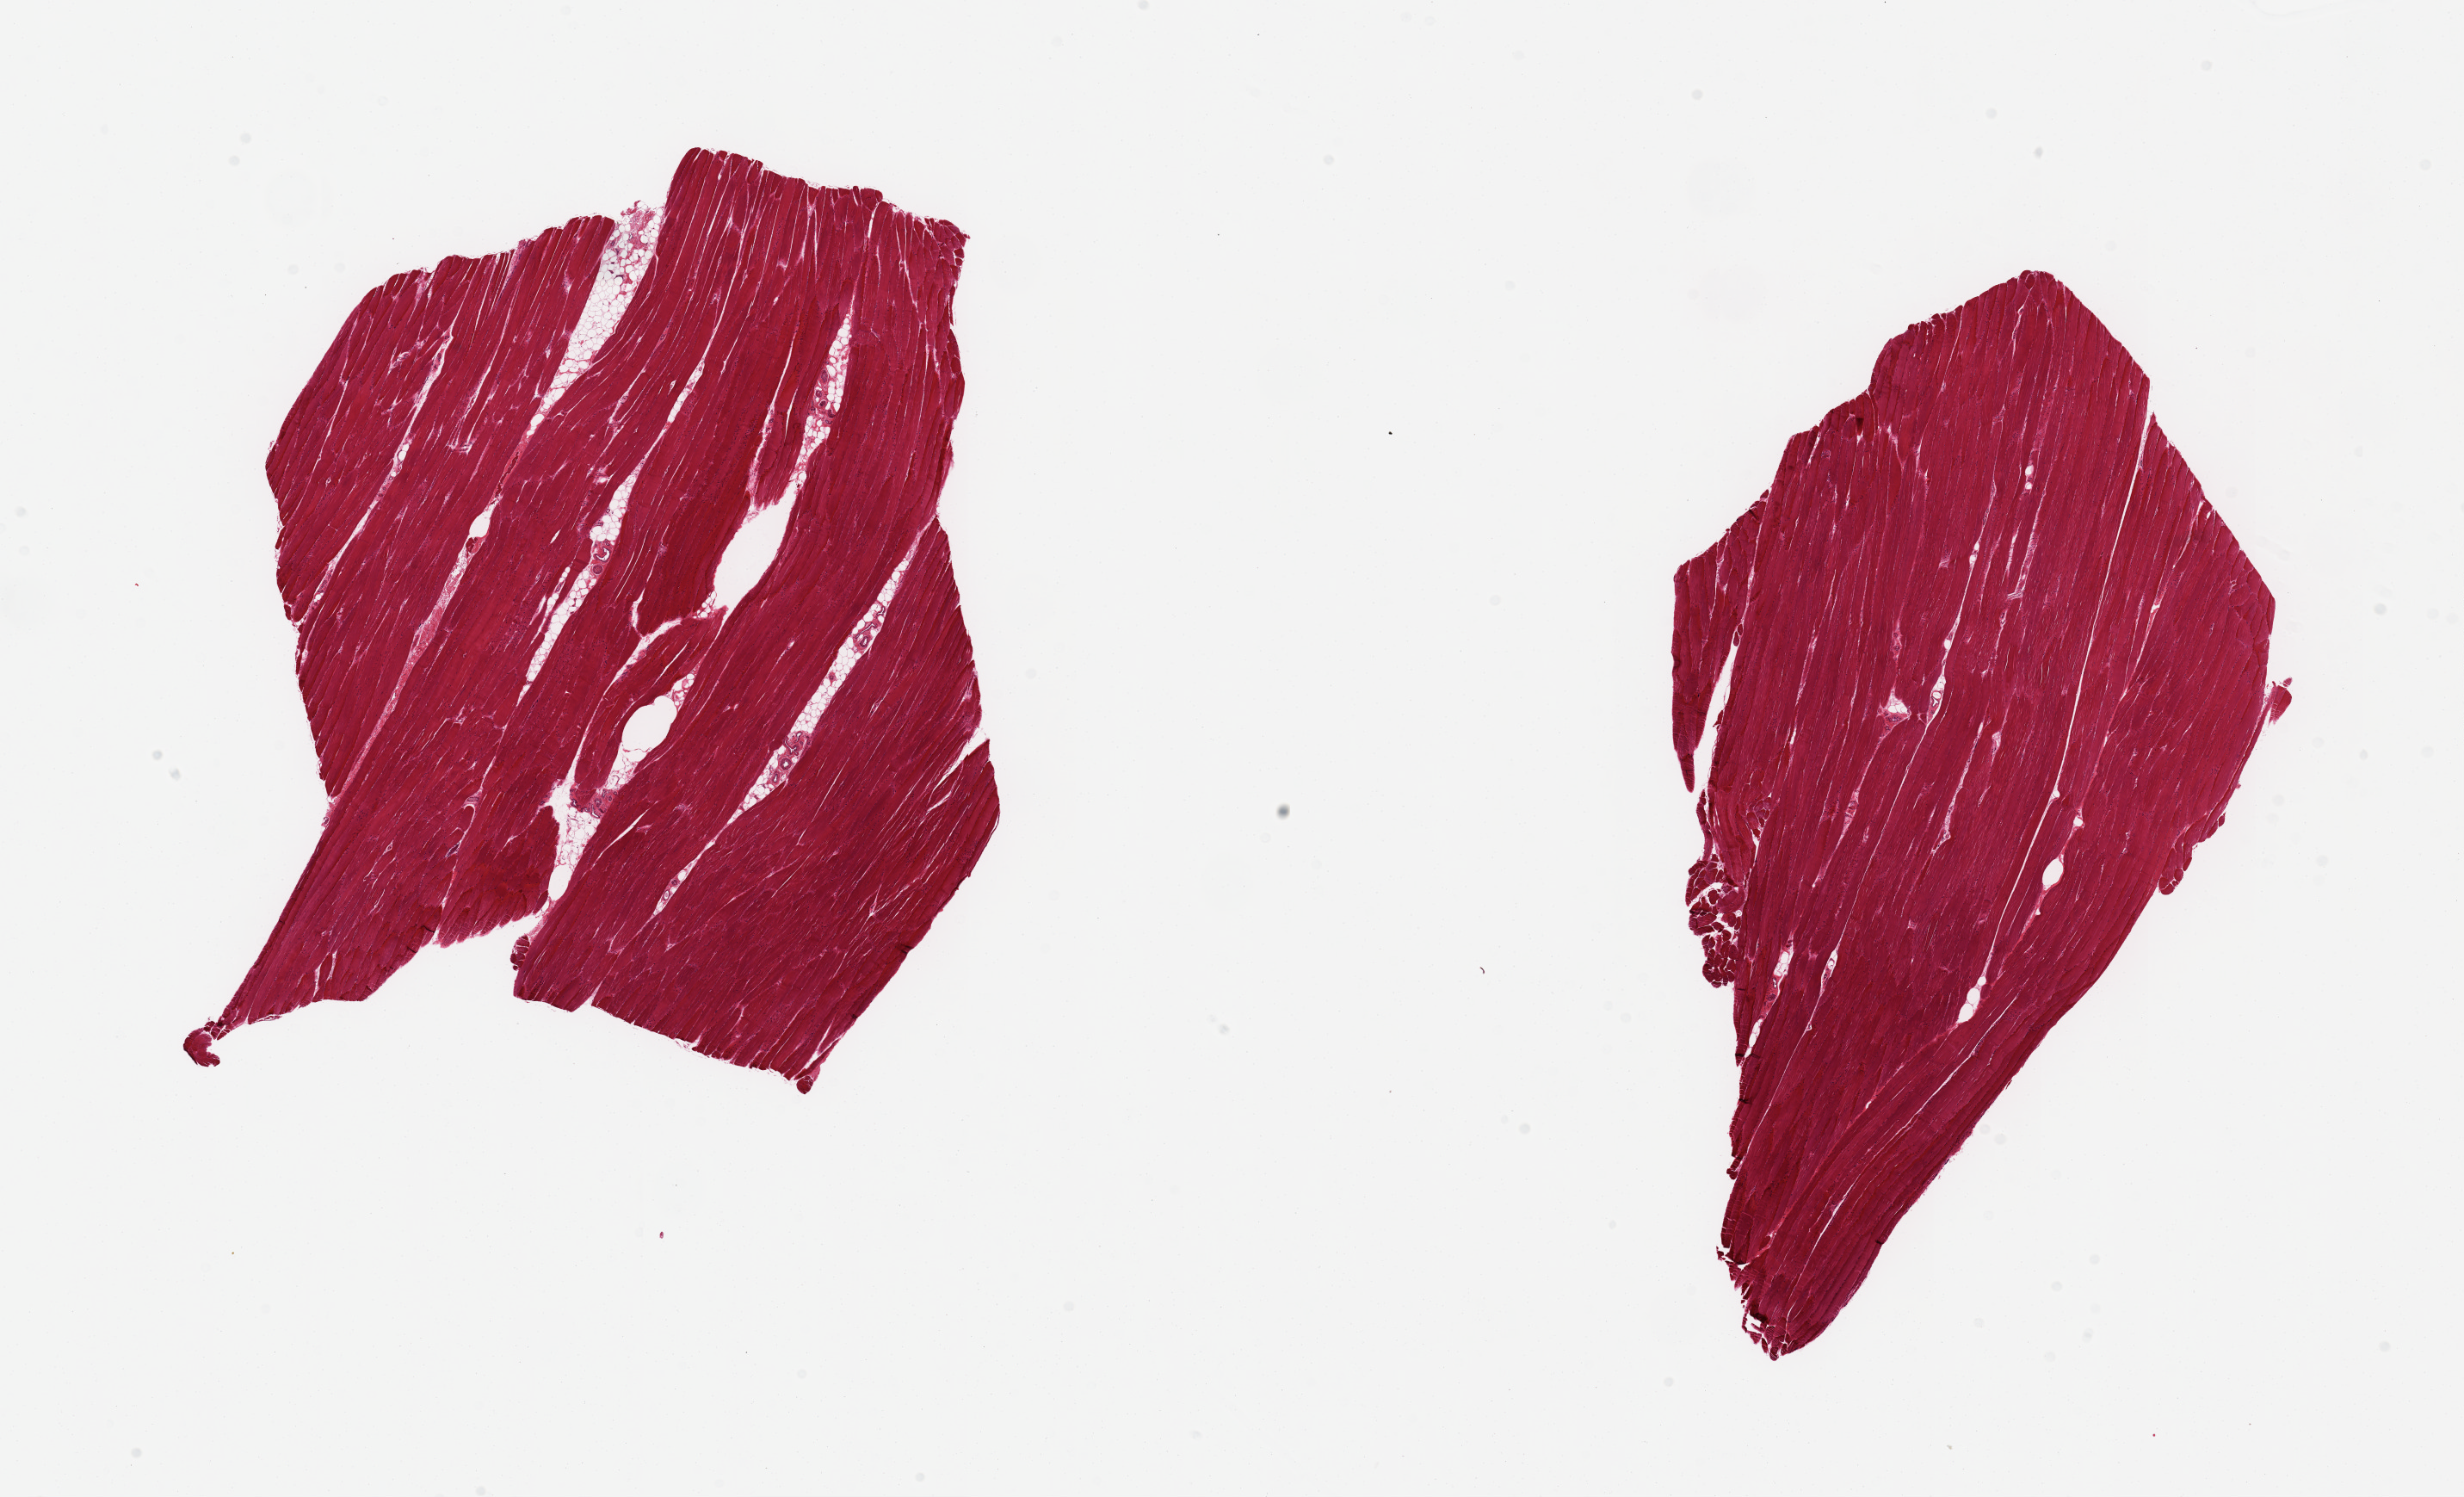
Whole-slide image, hematoxylin and eosin (H&E) stain, low-resolution overview of the scanned area, about 22.6 x 13.8 mm (from a 20x scan), PAXgene-fixed paraffin-embedded (PFPE) section, sampled site (target tissue): skeletal muscle, donor tissue sample. Donor: male.
Review note (as recorded): 2 pieces; one piece includes 5-10% internal fat.